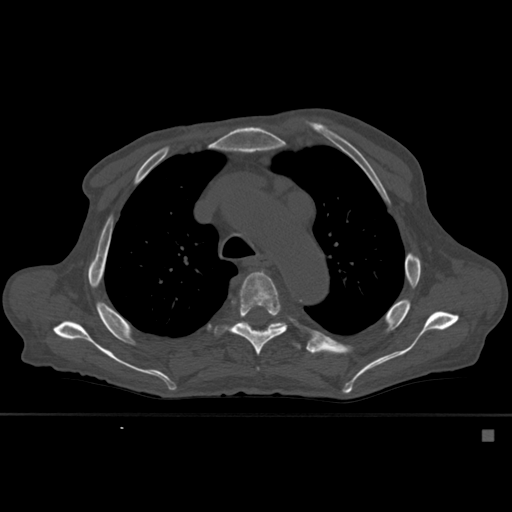
CT including the spine, one axial slice. Slice 401 of 527 in the series (ordered by position). Bone window (W 1800 / L 400 HU). 1.5 mm slice thickness. 512 × 512 image matrix, field of view 373 × 373 mm. Patient: male, 78 years. Case-level facts recorded for this patient, not image findings: primary cancer: prostate.
Annotated regions visible in this slice (semi-automatic segmentation, software-assisted and operator-edited):
- T5 vertebra: bounding box (x1, y1, x2, y2) in pixels: (231, 271, 288, 356)
- T6 vertebra: (272, 325, 301, 350)